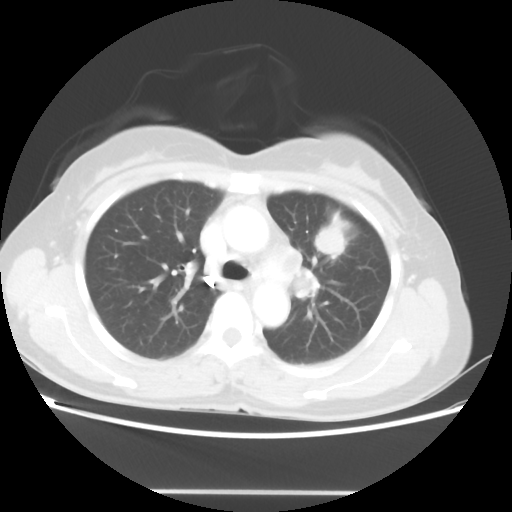
Chest CT, one axial slice; slice 31 of 46 in the series (ordered by position); reconstruction kernel STANDARD; 100 kVp; lung window (W 1500 / L -600 HU); 5 mm slice thickness; 512 × 512 image matrix, field of view 360 × 360 mm. Female patient, age 50 years. From the clinical record (not read from this slice): clinical TNM (as recorded): T1c N1 M0; histopathological grade: G3.
Structures marked on this image (bounding box drawn by a radiologist):
- lung tumour (recorded histology: adenocarcinoma): bounding box [x1, y1, x2, y2] px = [313, 214, 347, 257]